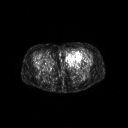
FDG PET of an extremity soft-tissue mass (from a PET/CT study), one axial slice; position 29 of 267 along the scan axis; 3.27 mm slice thickness; 128 × 128 image matrix, field of view 700 × 700 mm. Patient: female, 47 years. From the clinical record (not read from this slice): histological type: myxofibrosarcoma; grade: intermediate; site of the primary tumour: left thigh.
Annotated regions visible in this slice (expert contour drawn on MRI and transferred to this co-registered scan by the dataset authors):
- gross tumour volume including surrounding oedema: bounding box <65,51,83,65> (left, top, right, bottom; pixels)
- gross tumour volume (mass): <66,51,82,63>